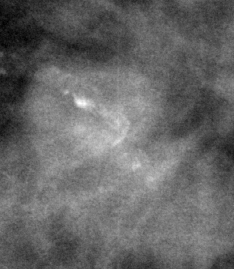
Crop from a digitized film mammogram around one marked abnormality; right breast; MLO view.
- Mass, shape architectural distortion, margins ill defined / spiculated; BI-RADS assessment category 4; pathology (as recorded): malignant.